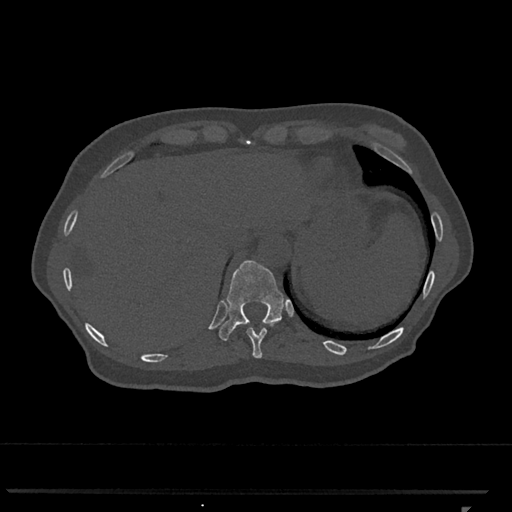
CT including the spine, one axial slice; bone window (W 1800 / L 400 HU); 0.5 mm slice thickness; 512 × 512 image matrix. Female patient, age 62 years. Case-level facts recorded for this patient, not image findings: primary cancer: renal.
Annotated regions visible in this slice (semi-automatic segmentation, software-assisted and operator-edited):
- T10 vertebra: bounding box (x1, y1, x2, y2) in pixels: (246, 327, 267, 359)
- T11 vertebra: (219, 260, 284, 341)